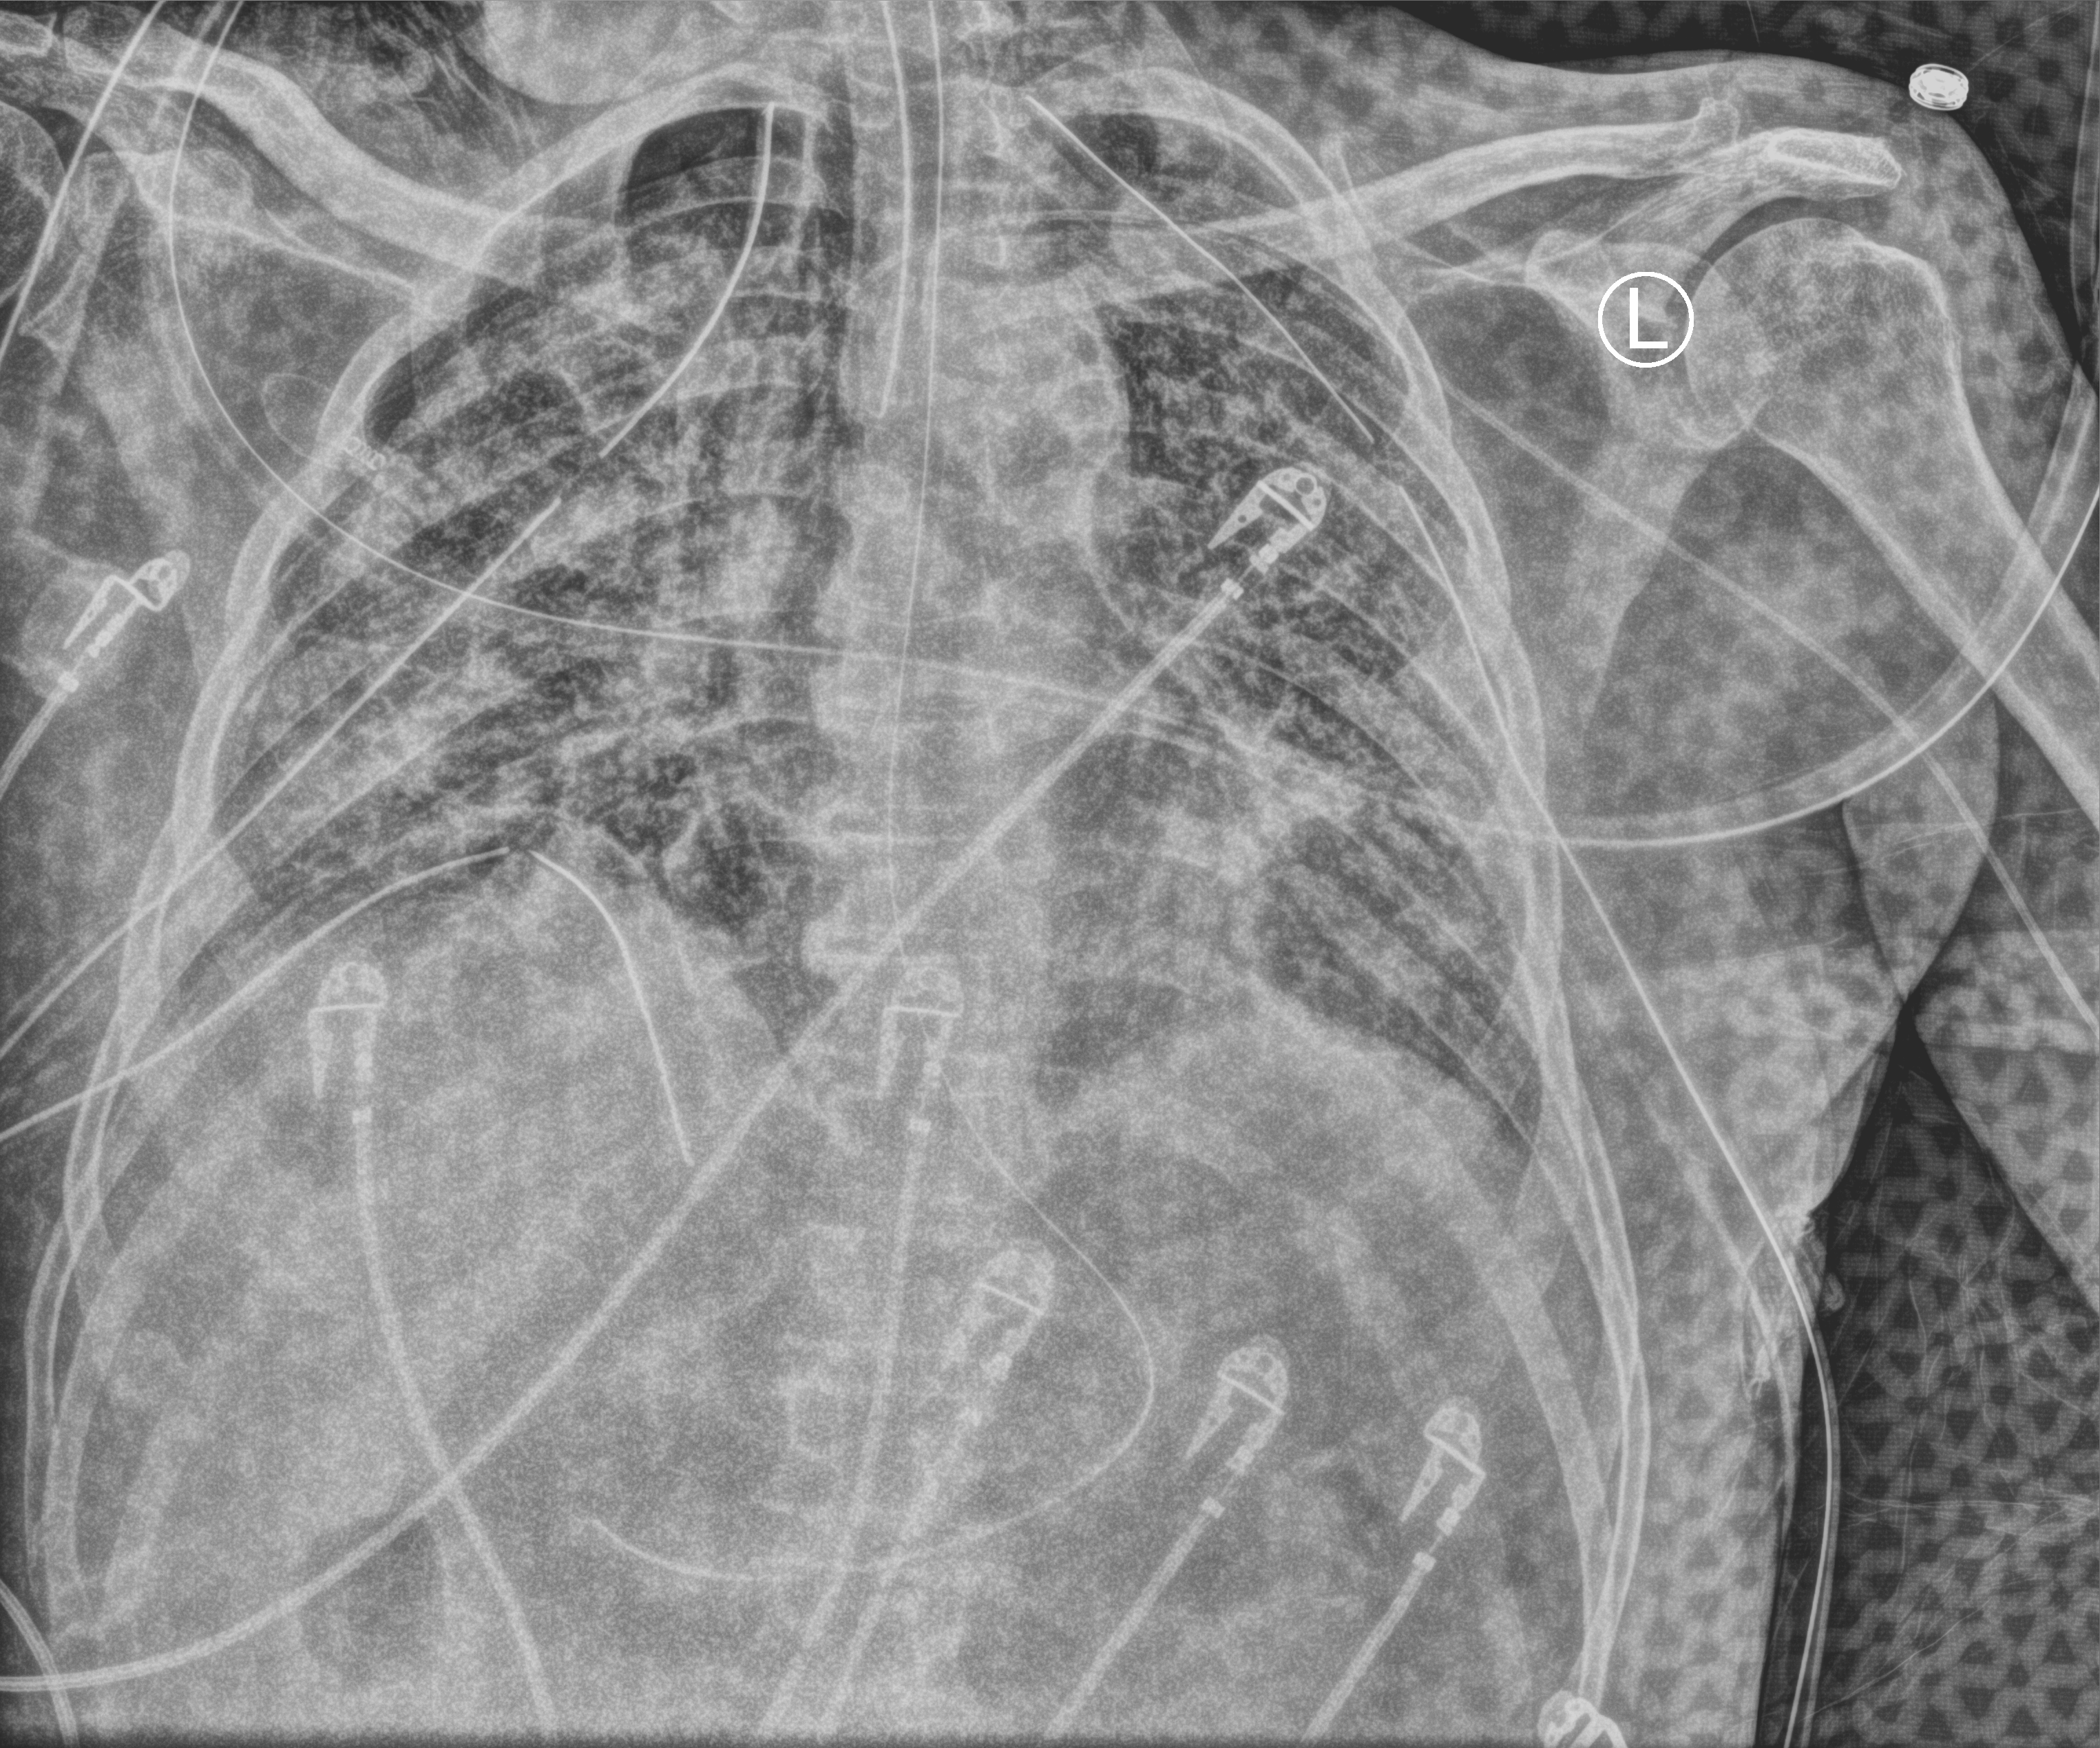
Bedside chest radiograph (computed radiography). Male patient hospitalised with COVID-19, age 18–59 years.
From the hospital-stay record, not from the radiograph (when in the stay this image was taken is not recorded): admitted to intensive care during this hospital stay: yes; mechanically ventilated during this hospital stay: yes.